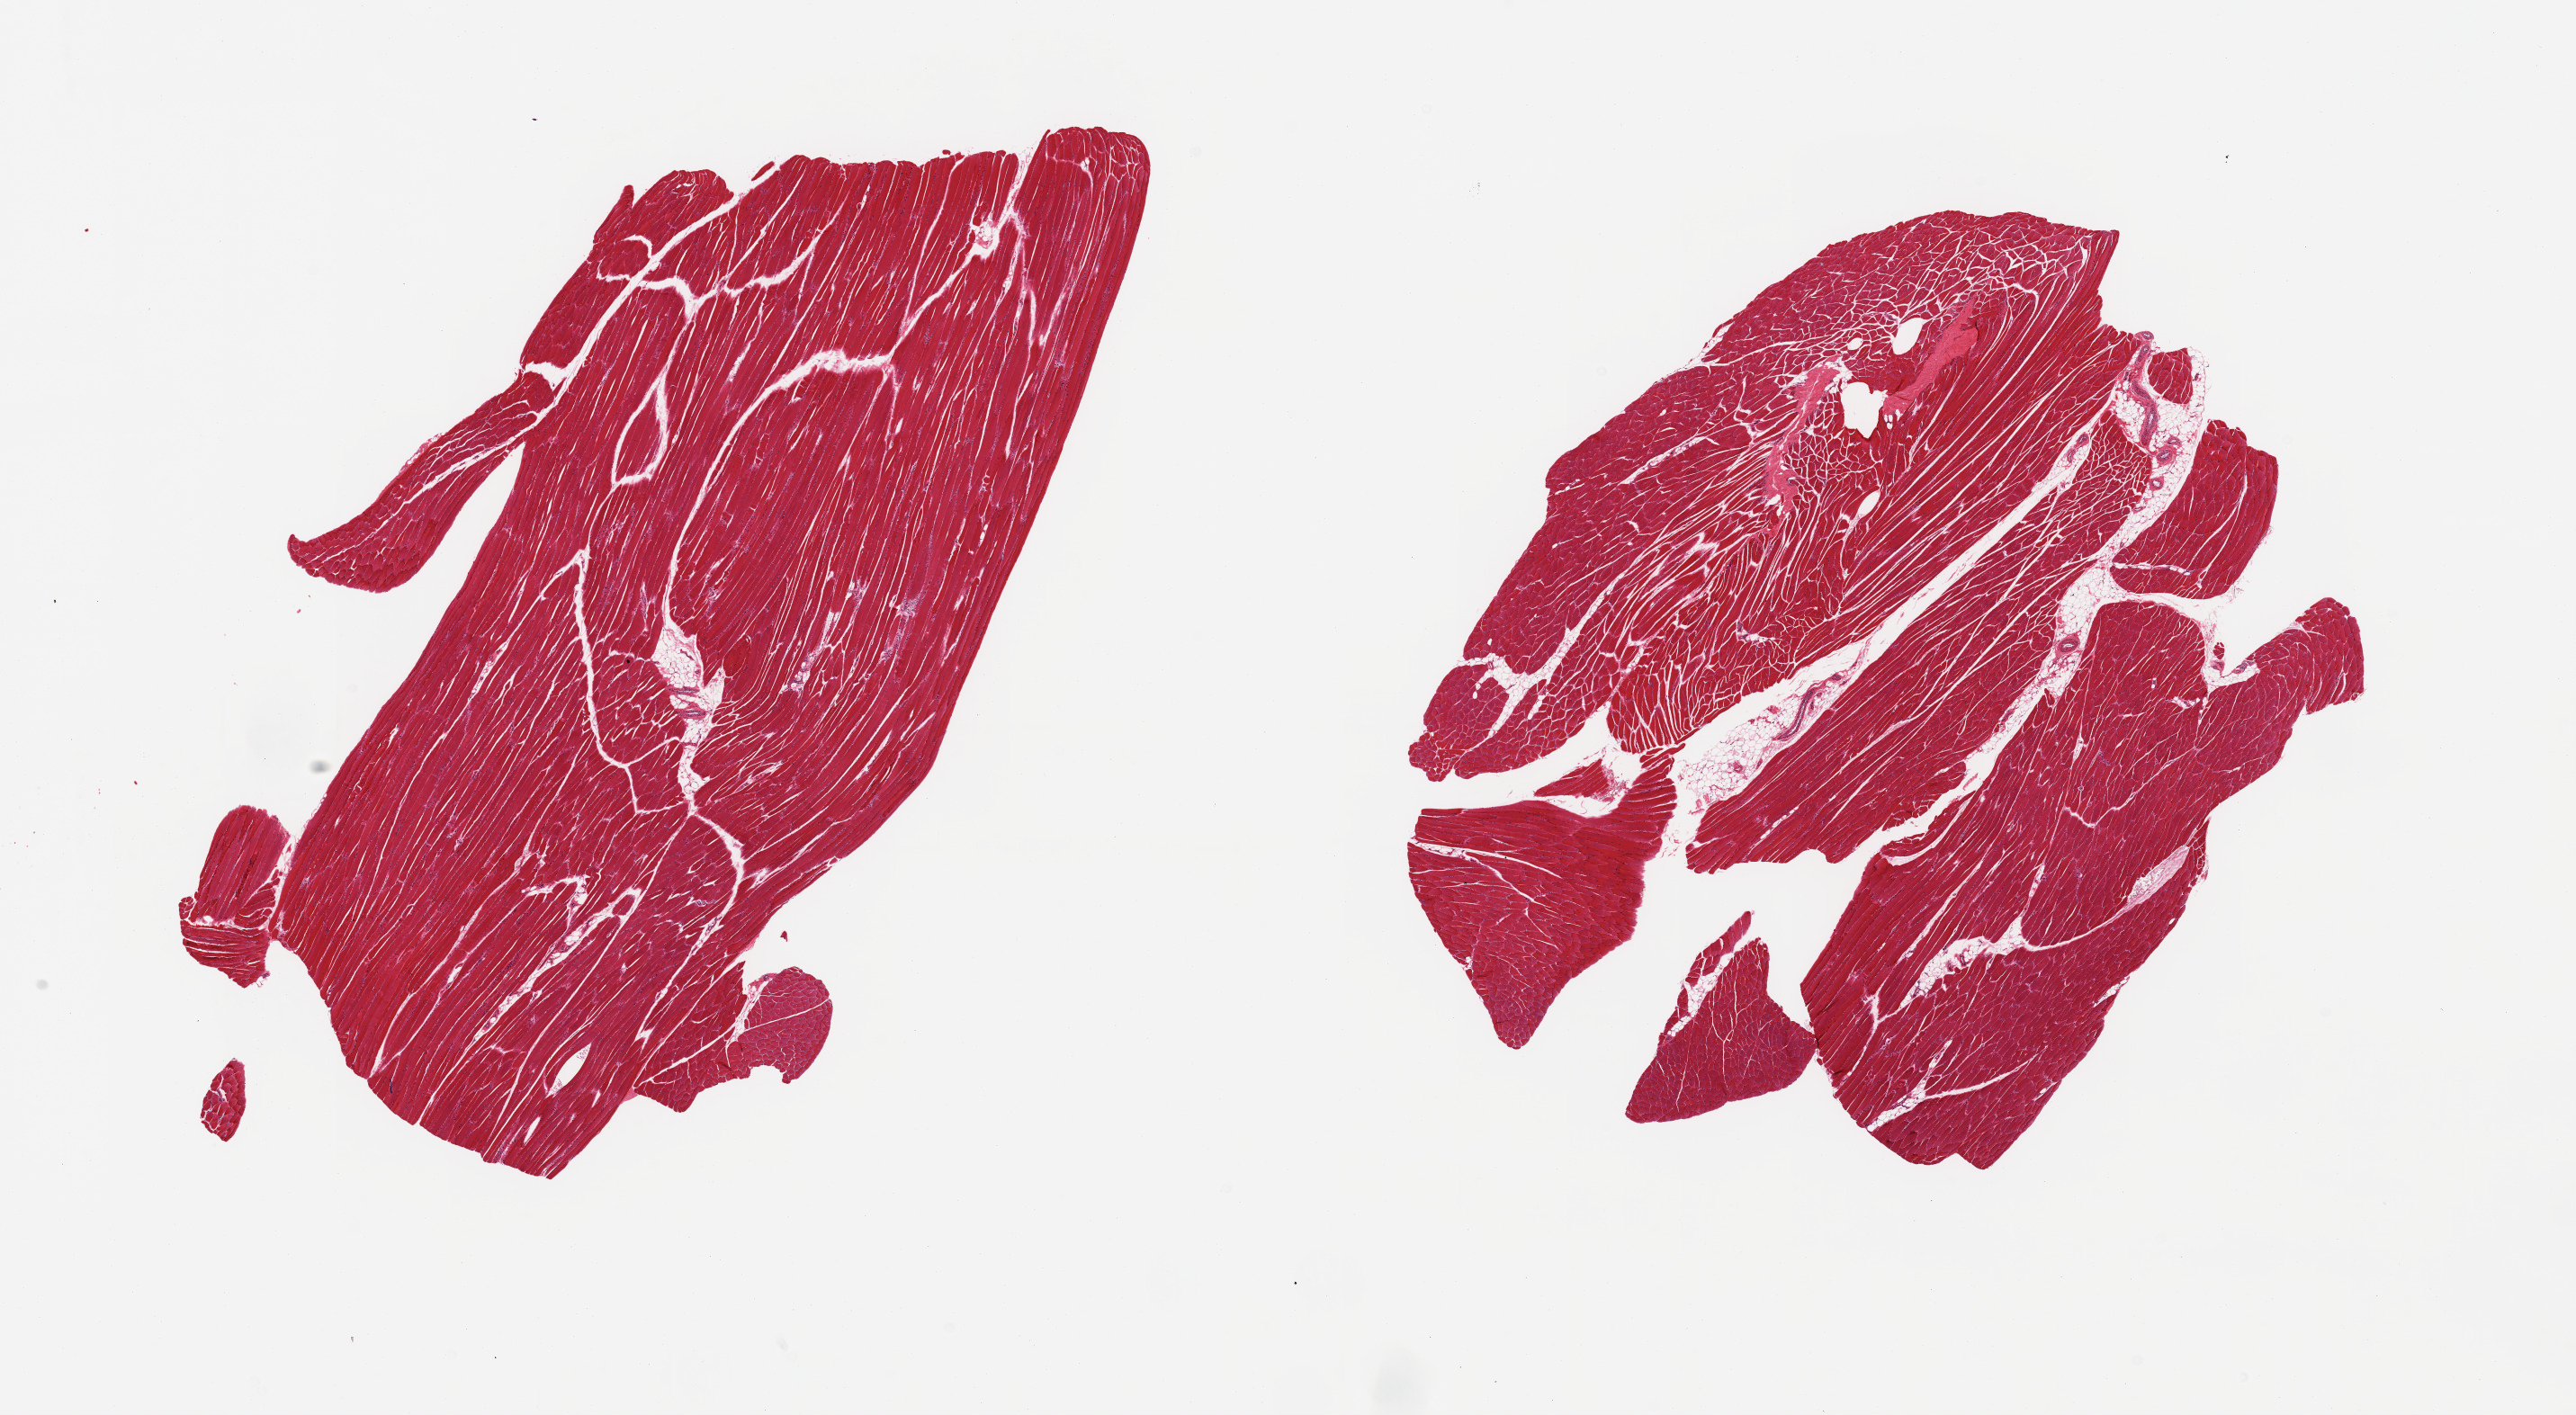
Digitized haematoxylin and eosin-stained section, low-resolution overview of the scanned area, about 22.6 x 12.4 mm (from a 20x scan). PAXgene-fixed paraffin-embedded (PFPE) section. Target tissue: skeletal muscle. Donor tissue sample. Female donor.
• reviewer comment on this tissue sample: 2 pieces; minimal internal fat content